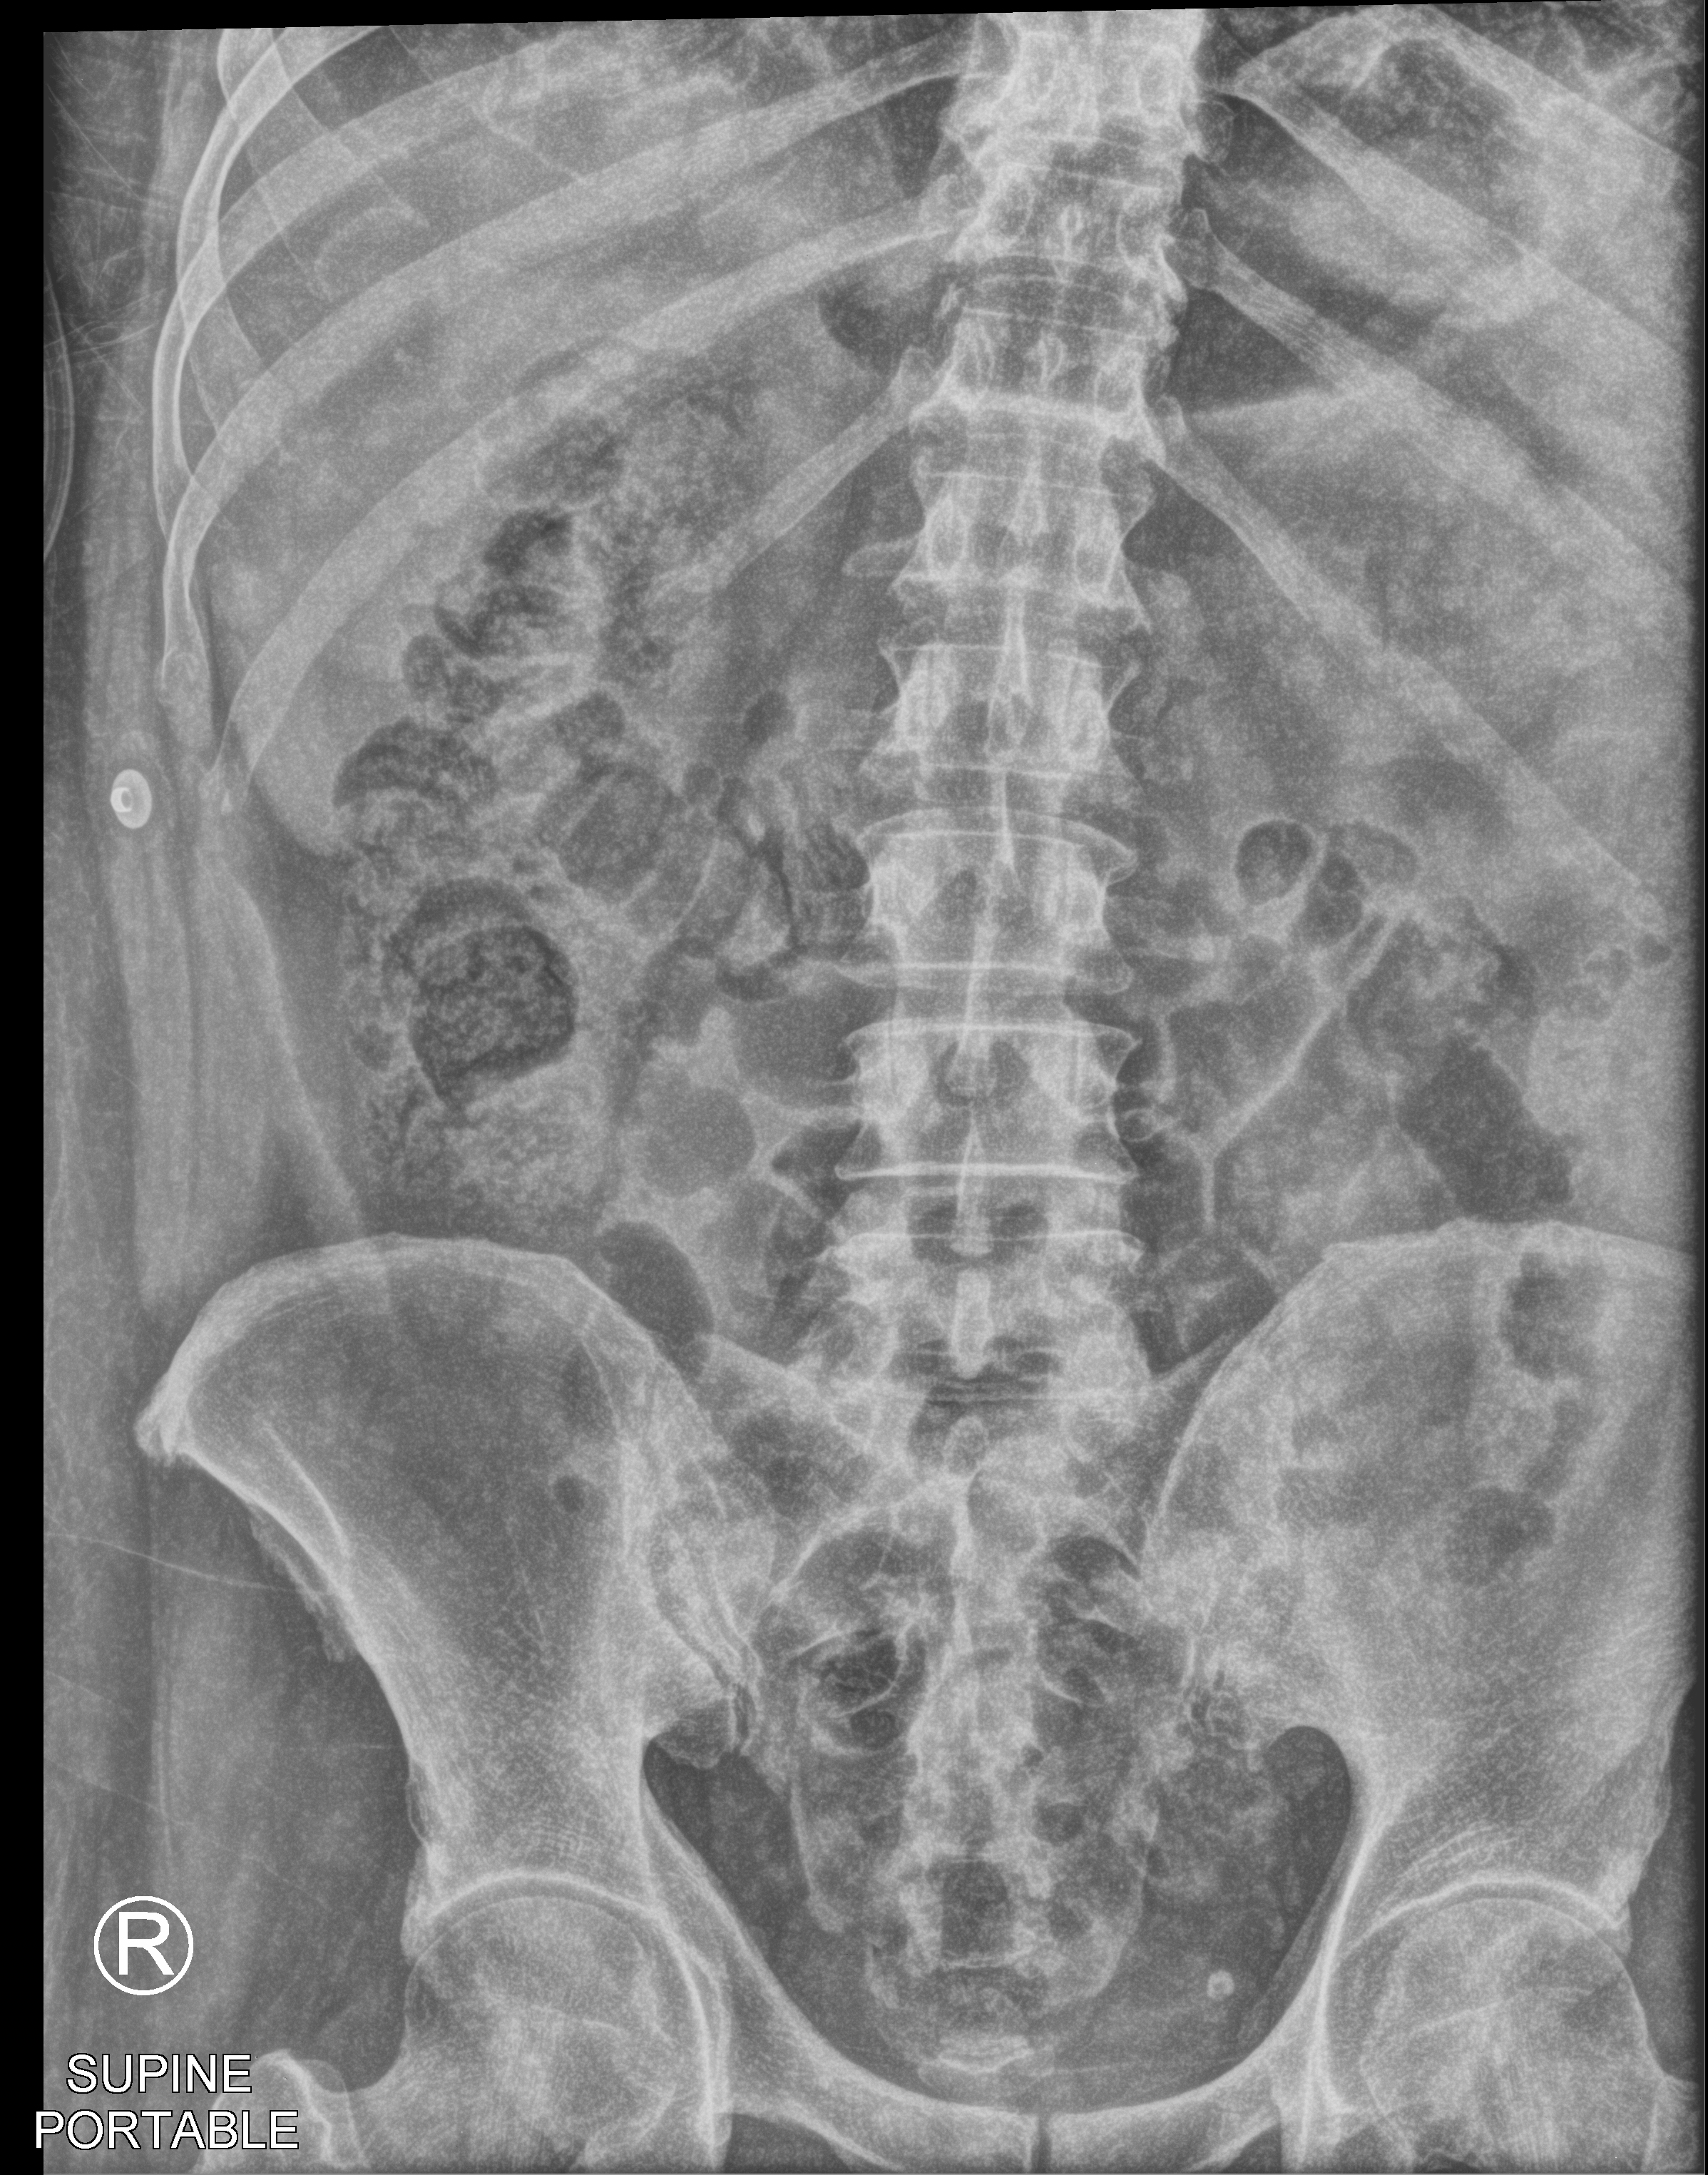
Portable abdomen radiograph, anteroposterior (AP) projection. Male patient hospitalised with COVID-19, age 18–59 years.
Admission-level facts for this patient (not findings on this image; timing relative to this image not recorded): diabetes (admission record): no.